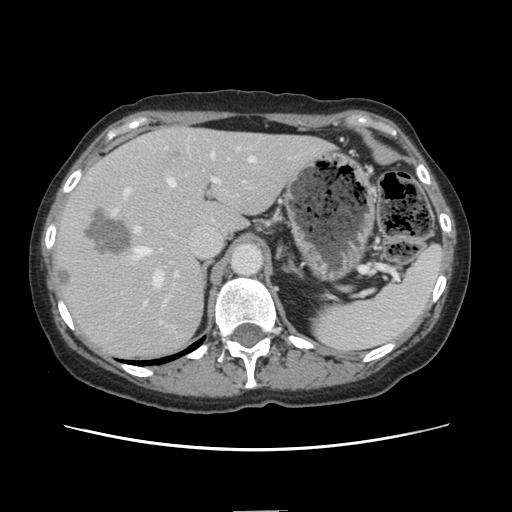
Contrast-enhanced abdominal CT, one axial slice; slice 97 of 141 in the series (ordered by position); soft-tissue window (W 400 / L 40 HU); 2.5 mm slice thickness; 512 × 512 image matrix, field of view 350 × 350 mm. Female patient, age 63 years. From the clinical record (not read from this slice): diagnosis: colorectal cancer liver metastases, imaged before liver resection; multiple liver metastases: yes; largest metastasis: 3.2 cm; chemotherapy before resection: yes.
Structures marked on this image (manually delineated by an expert):
- hepatic veins: bounding box (x1, y1, x2, y2) in pixels: (135, 154, 255, 285)
- liver: (51, 128, 330, 361)
- planned liver remnant (the part of the liver to remain after resection): (184, 129, 330, 237)
- portal vein (with intrahepatic branches): (113, 150, 243, 308)